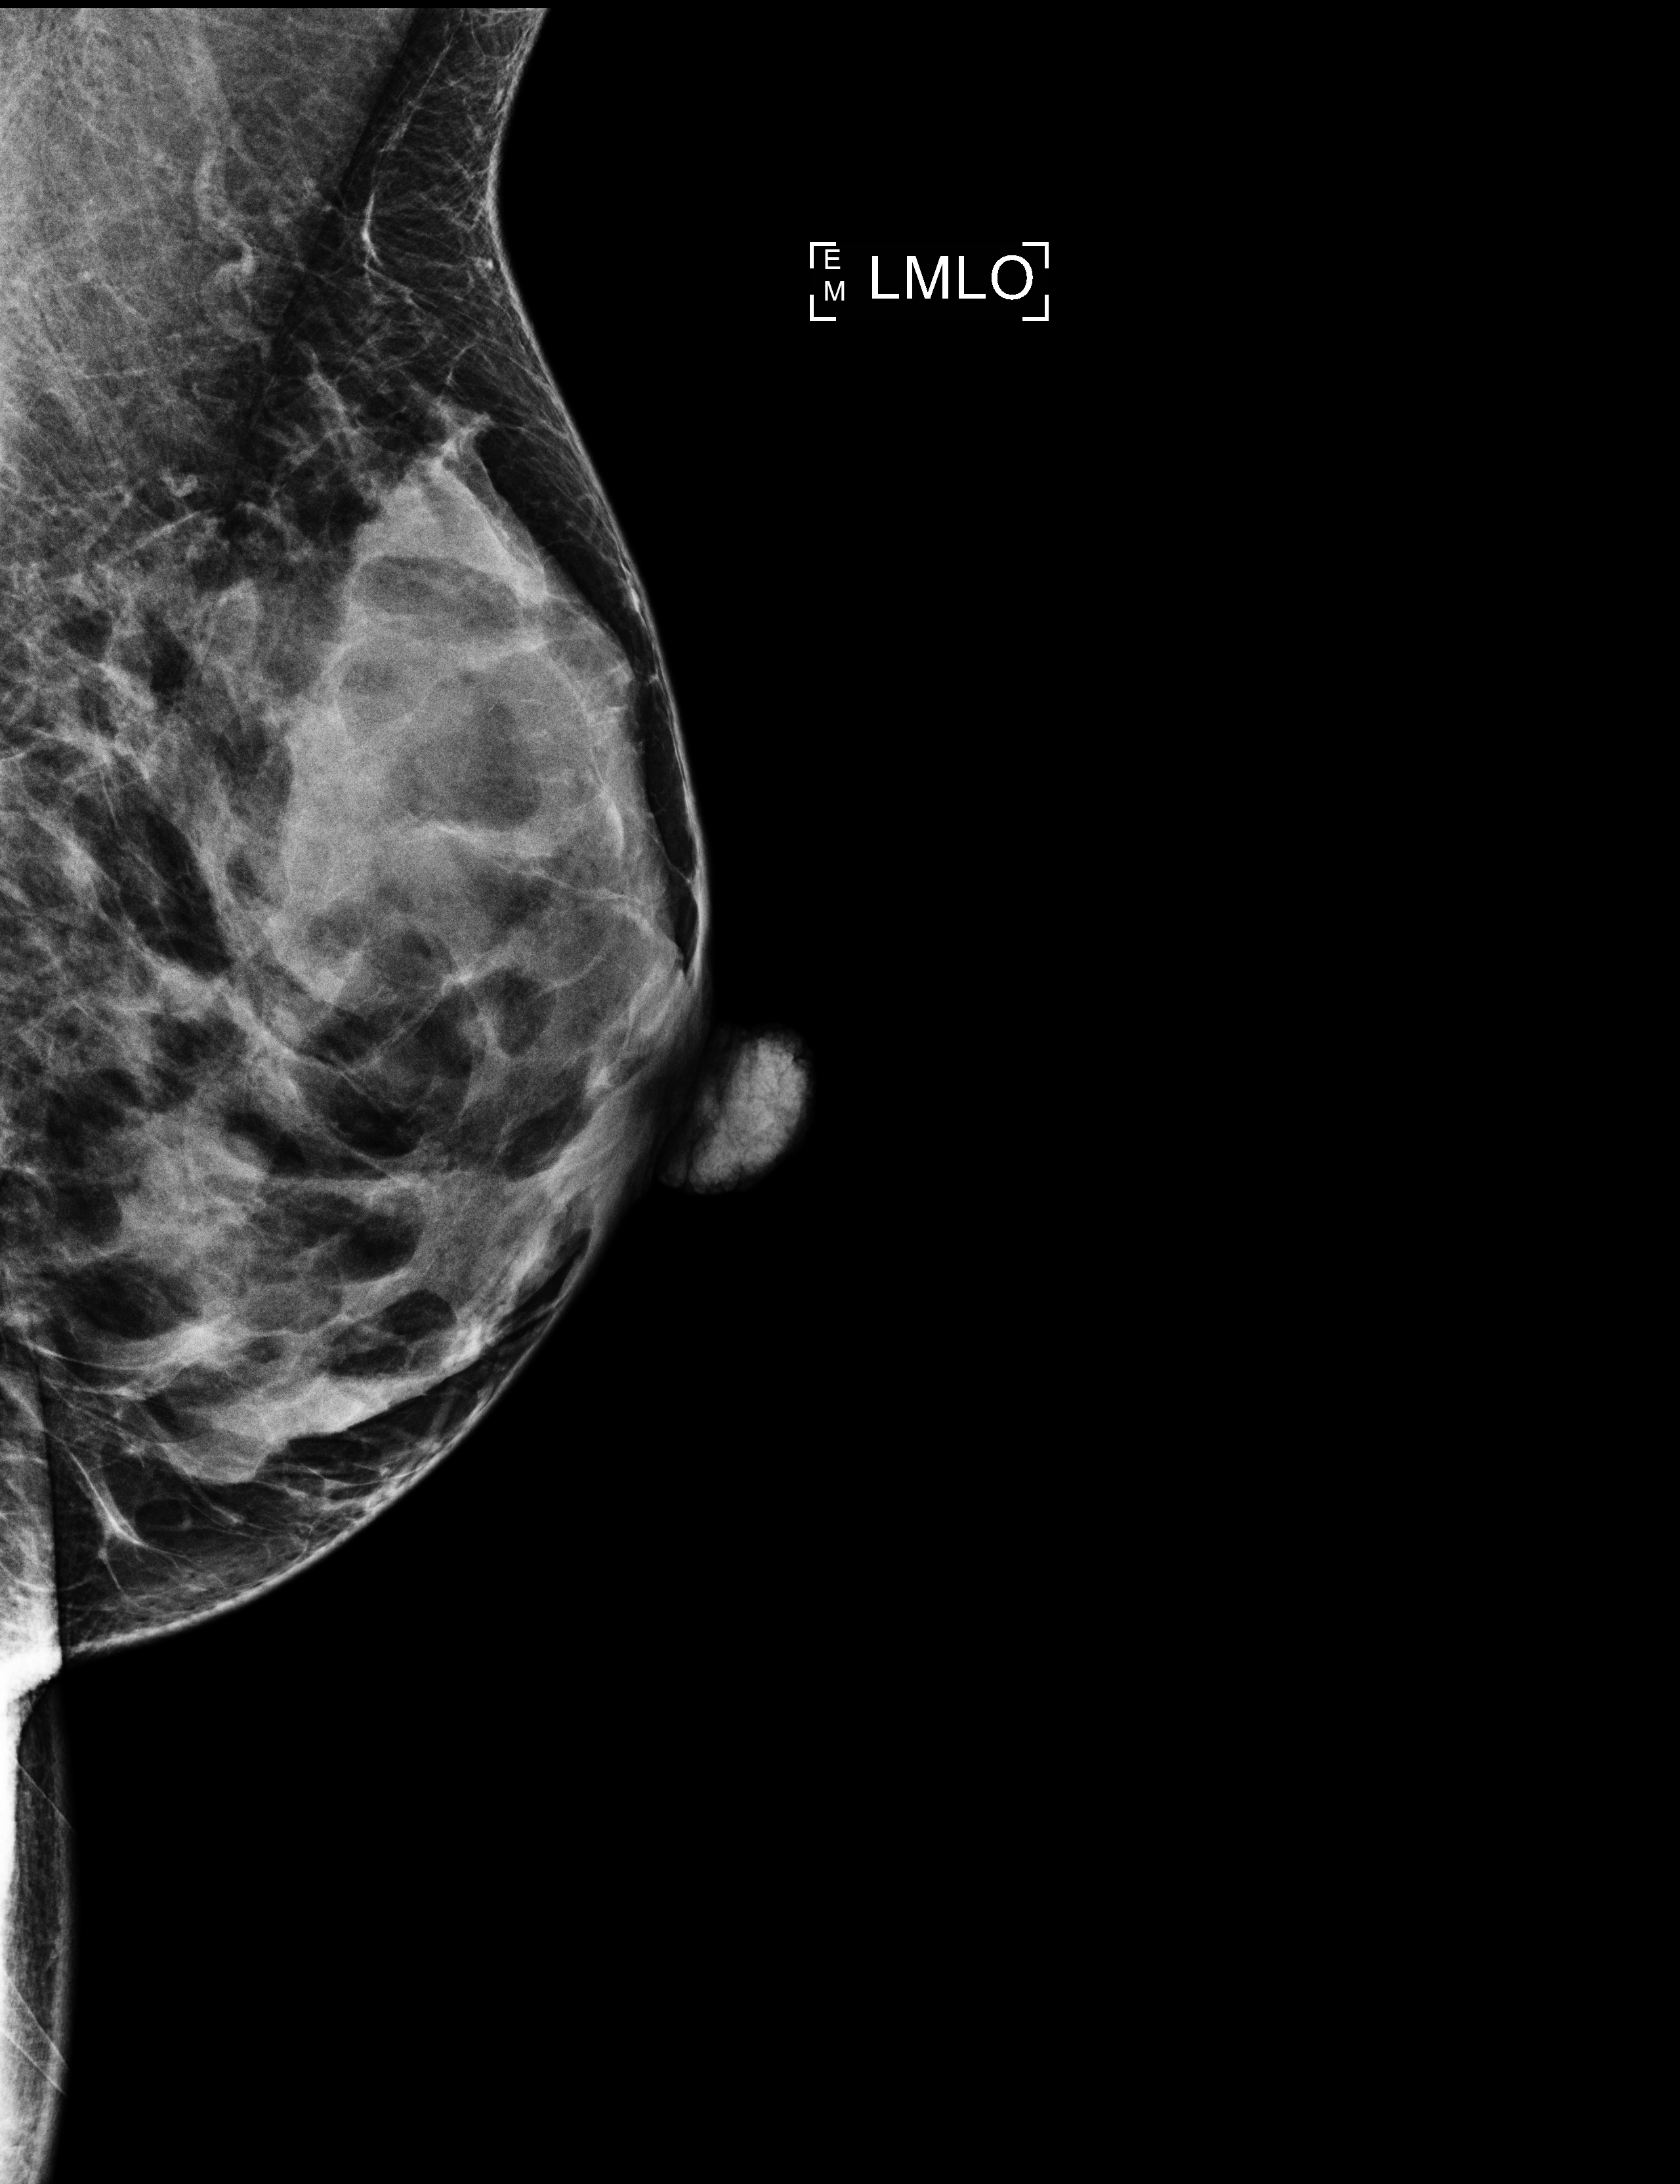
Digital mammogram (FFDM), left breast, MLO view, screening examination, compressed breast thickness 42 mm, system: Selenia Dimensions. Patient aged 42 years (female).
- BI-RADS breast density category at the screening exam (both breasts, scale 1–4): 4
- final BI-RADS category for the screening round (tomosynthesis exam, both breasts): category 2
- recall: recalled for additional imaging after this screen